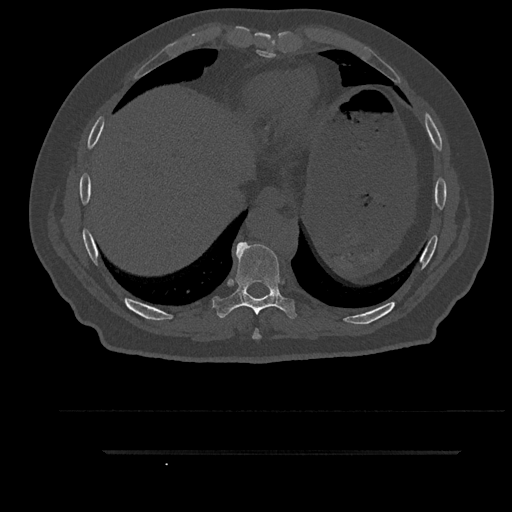
CT including the spine, one axial slice; position 428 of 797 along the scan axis; reconstruction kernel Br40s/3; bone window (W 1800 / L 400 HU); 512 × 512 image matrix, field of view 432 × 432 mm. Male patient, age 63 years. Case-level facts recorded for this patient, not image findings: primary cancer: renal.
Structures marked on this image (semi-automatically segmented with operator editing):
- T8 vertebra: bounding box <252,329,261,339> (left, top, right, bottom; pixels)
- T9 vertebra: <212,242,296,319>